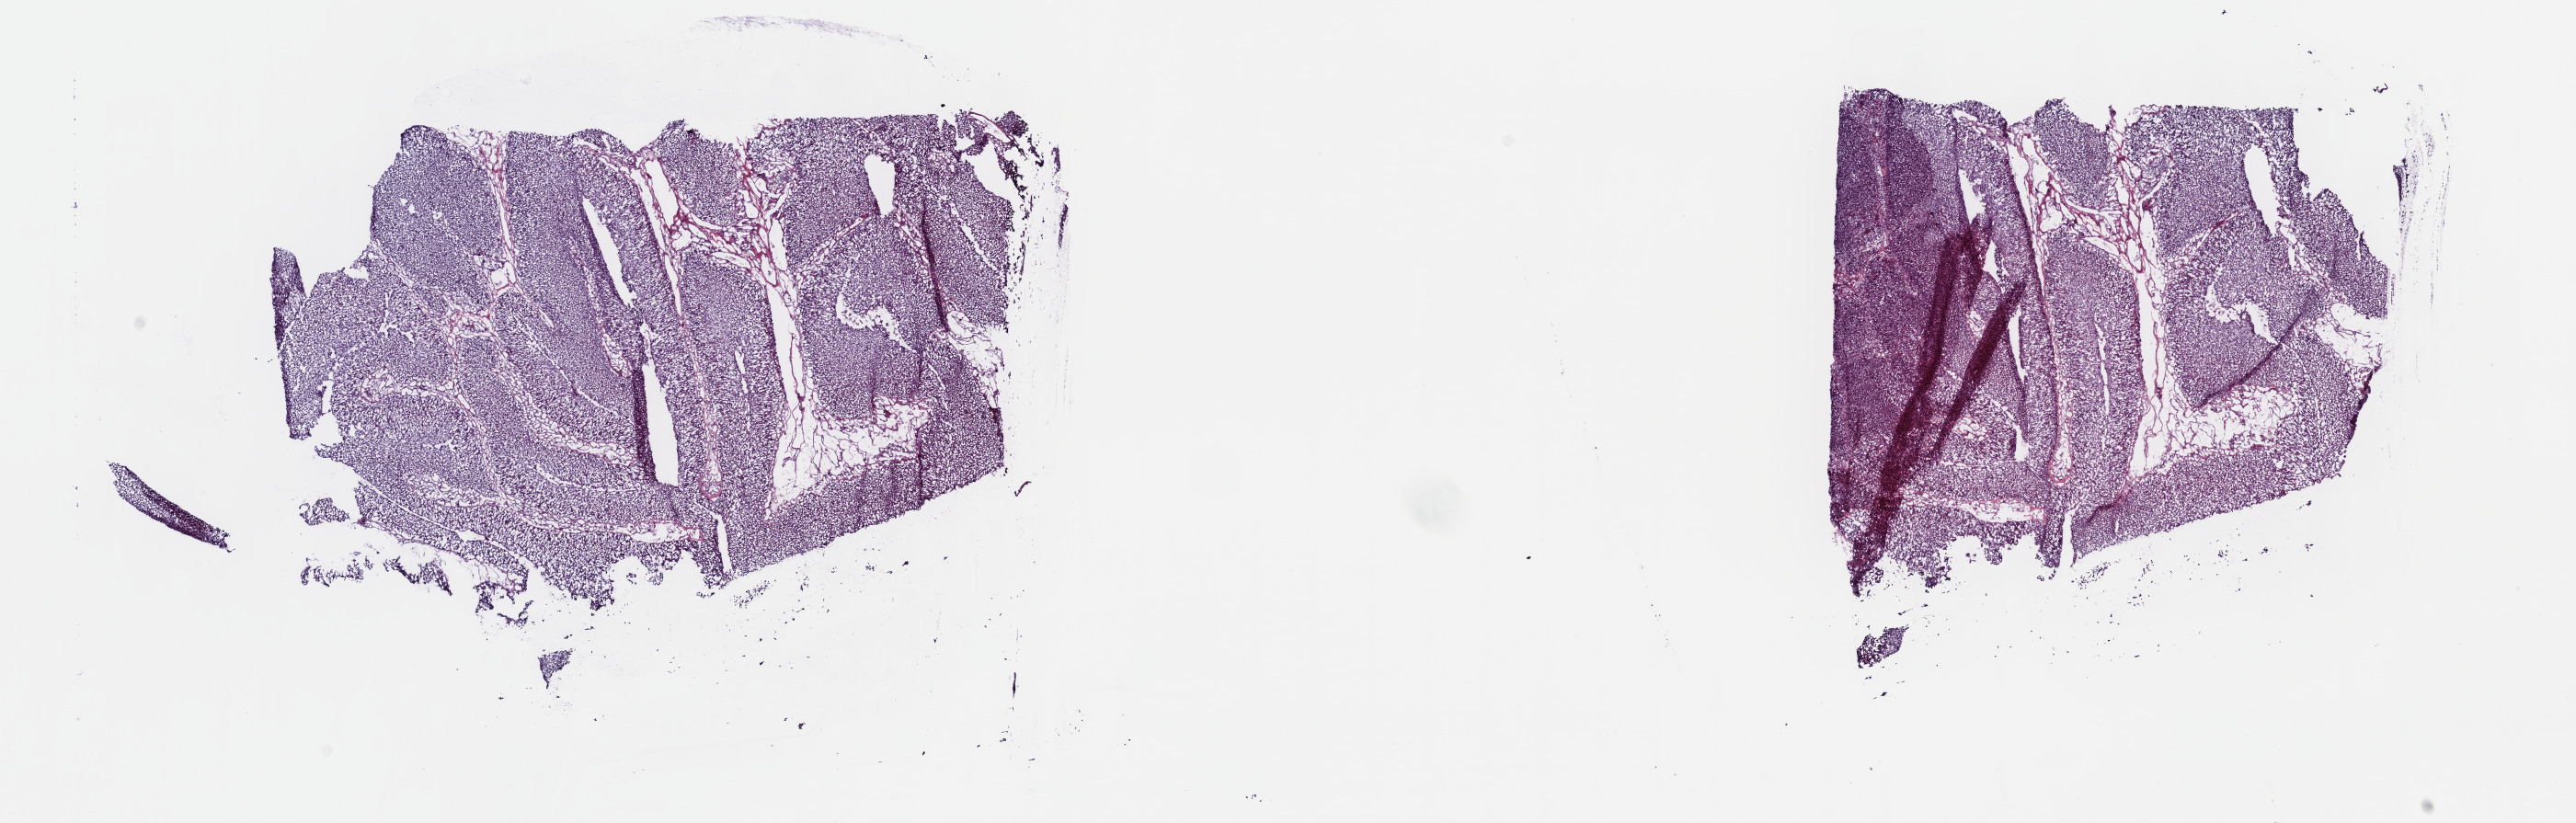
Digitized H&E tissue section (whole slide) — whole scanned area (about 22.7 x 7.2 mm, acquisition: 40x scan) shown as a low-resolution overview; frozen section from the top of the tissue portion; primary tumour sample from the bladder. Male patient; age at initial diagnosis 70 years. Pathologist review of this section (percent, as recorded): tumour cells 100%, tumour nuclei 98%.
Diagnosis: Transitional cell carcinoma.